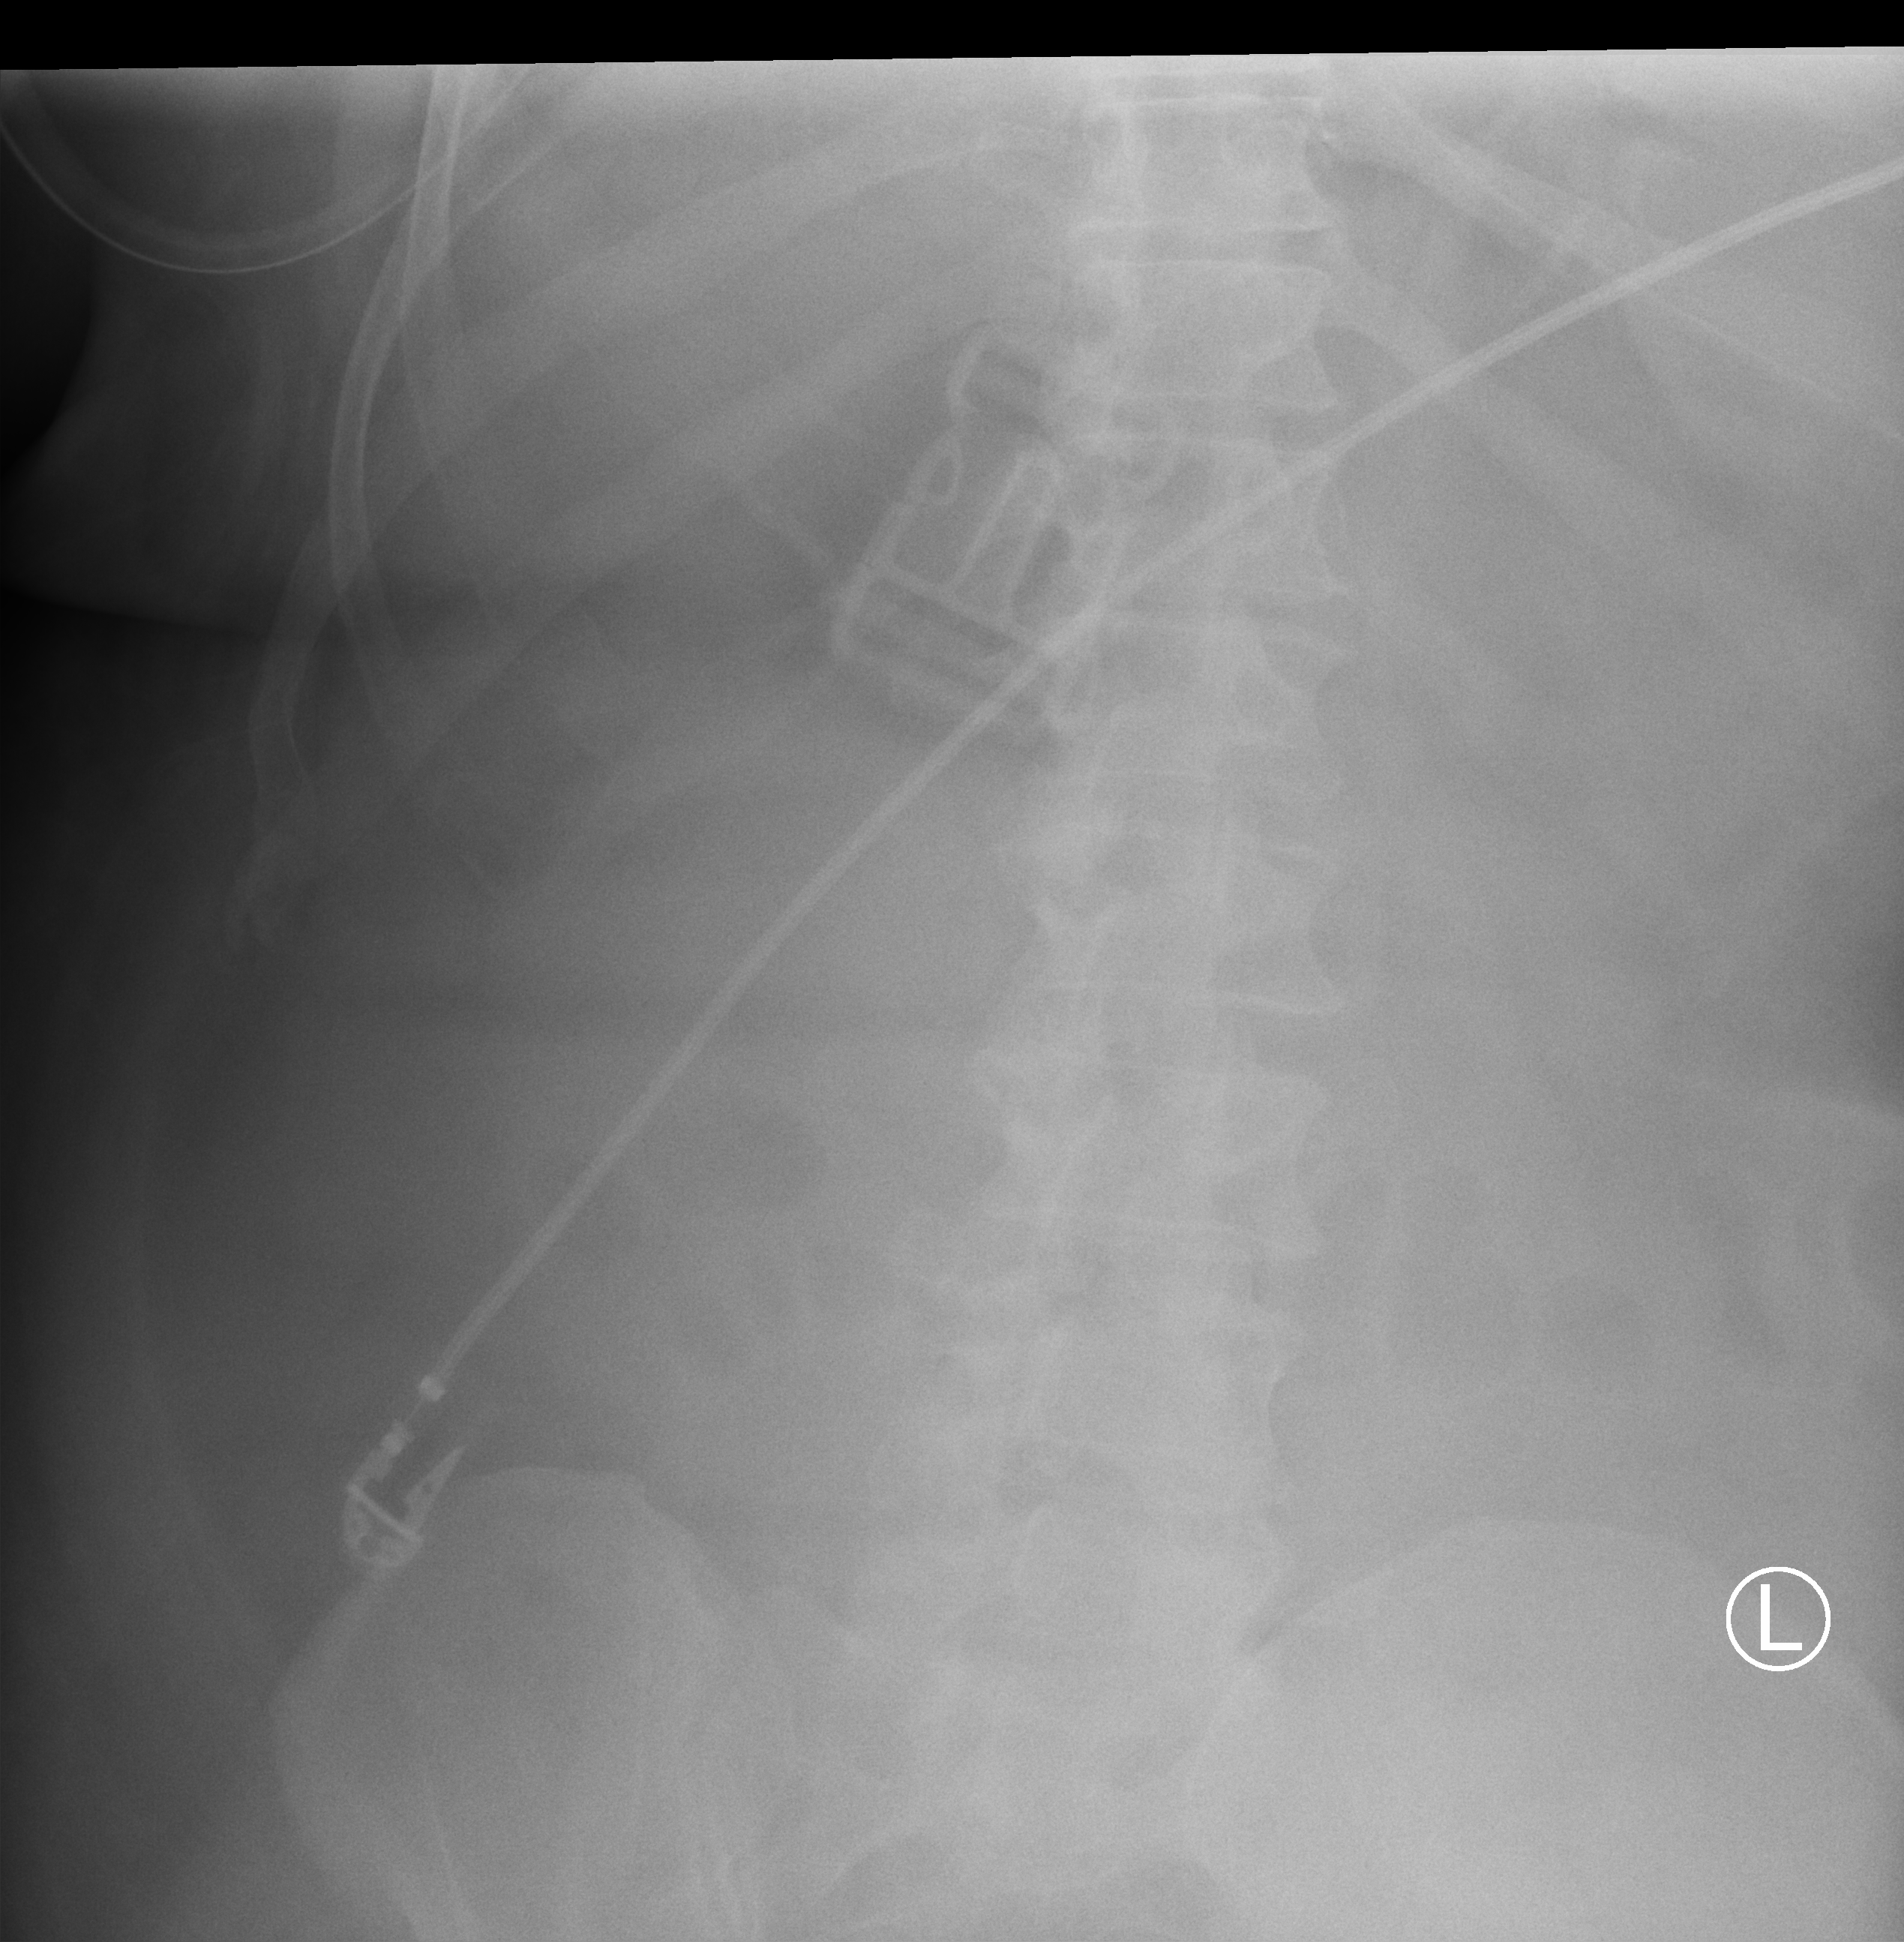
Abdomen X-ray (portable); anteroposterior (AP) projection. Patient hospitalised with COVID-19, aged 18–59 years.
From the hospital-stay record, not from the radiograph (when in the stay this image was taken is not recorded): mechanically ventilated during this hospital stay: yes.